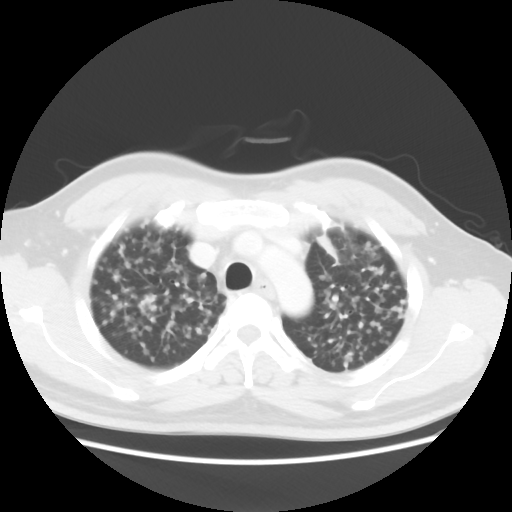
Chest CT, one axial slice. Slice 31 of 40 in the series (ordered by position). Reconstruction kernel STANDARD. 120 kVp. Lung window (W 1500 / L -600 HU). 512 × 512 image matrix, field of view 366 × 366 mm. Male patient, age 41 years. Case-level facts recorded for this patient, not image findings: clinical TNM (as recorded): T1c N3 M1b.
Outlined on this slice (rectangle marked by the reading radiologist):
- lung tumour (recorded histology: adenocarcinoma): bounding box (x1, y1, x2, y2) in pixels: (310, 228, 344, 268)